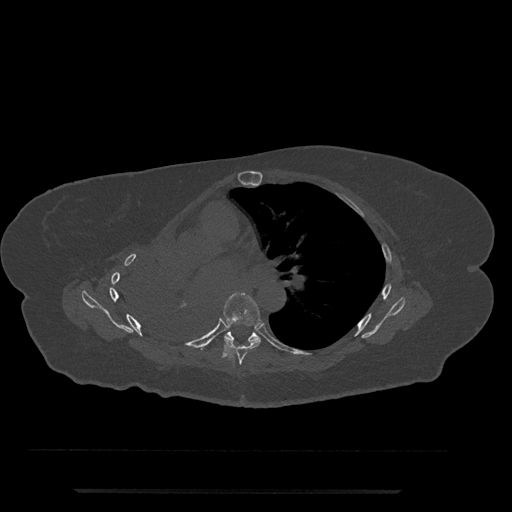
CT including the spine, one axial slice; slice 475 of 797 in the series (ordered by position); reconstruction kernel Br40s/3; 120 kVp; bone window (W 1800 / L 400 HU); 512 × 512 image matrix, field of view 440 × 440 mm. Patient: female, 51 years. From the clinical record (not read from this slice): primary cancer: neuro; vertebrae with lytic lesions (as recorded): T8.
Annotated regions visible in this slice (semi-automatic segmentation, software-assisted and operator-edited):
- T6 vertebra: bounding box (x1, y1, x2, y2) in pixels: (223, 292, 261, 365)
- T7 vertebra: (224, 331, 261, 341)